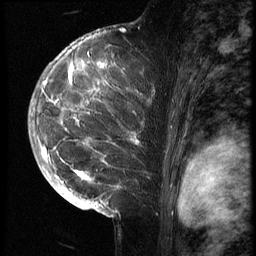
Breast MRI (dynamic contrast-enhanced), one sagittal slice; position 41 of 70 along the scan axis; 3 images stored at this slice position (order not interpretable as contrast timing); 1.5 T; TE 4.2 ms, TR 9 ms; 2.5 mm slice thickness; 256 × 256 image matrix, field of view 180 × 180 mm. Patient: female, 28 years. Case-level facts recorded for this patient, not image findings: setting: breast cancer imaged before/during neoadjuvant chemotherapy.
Annotated regions visible in this slice (semi-automatically segmented with operator editing):
- analysis volume of interest (the breast-tissue region the enhancement analysis was run in; not a lesion): bounding box <43,42,160,215> (left, top, right, bottom; pixels)
- tumour enhancement mask (voxels above the 140 % enhancement threshold inside the analysis volume of interest): <43,46,139,207>